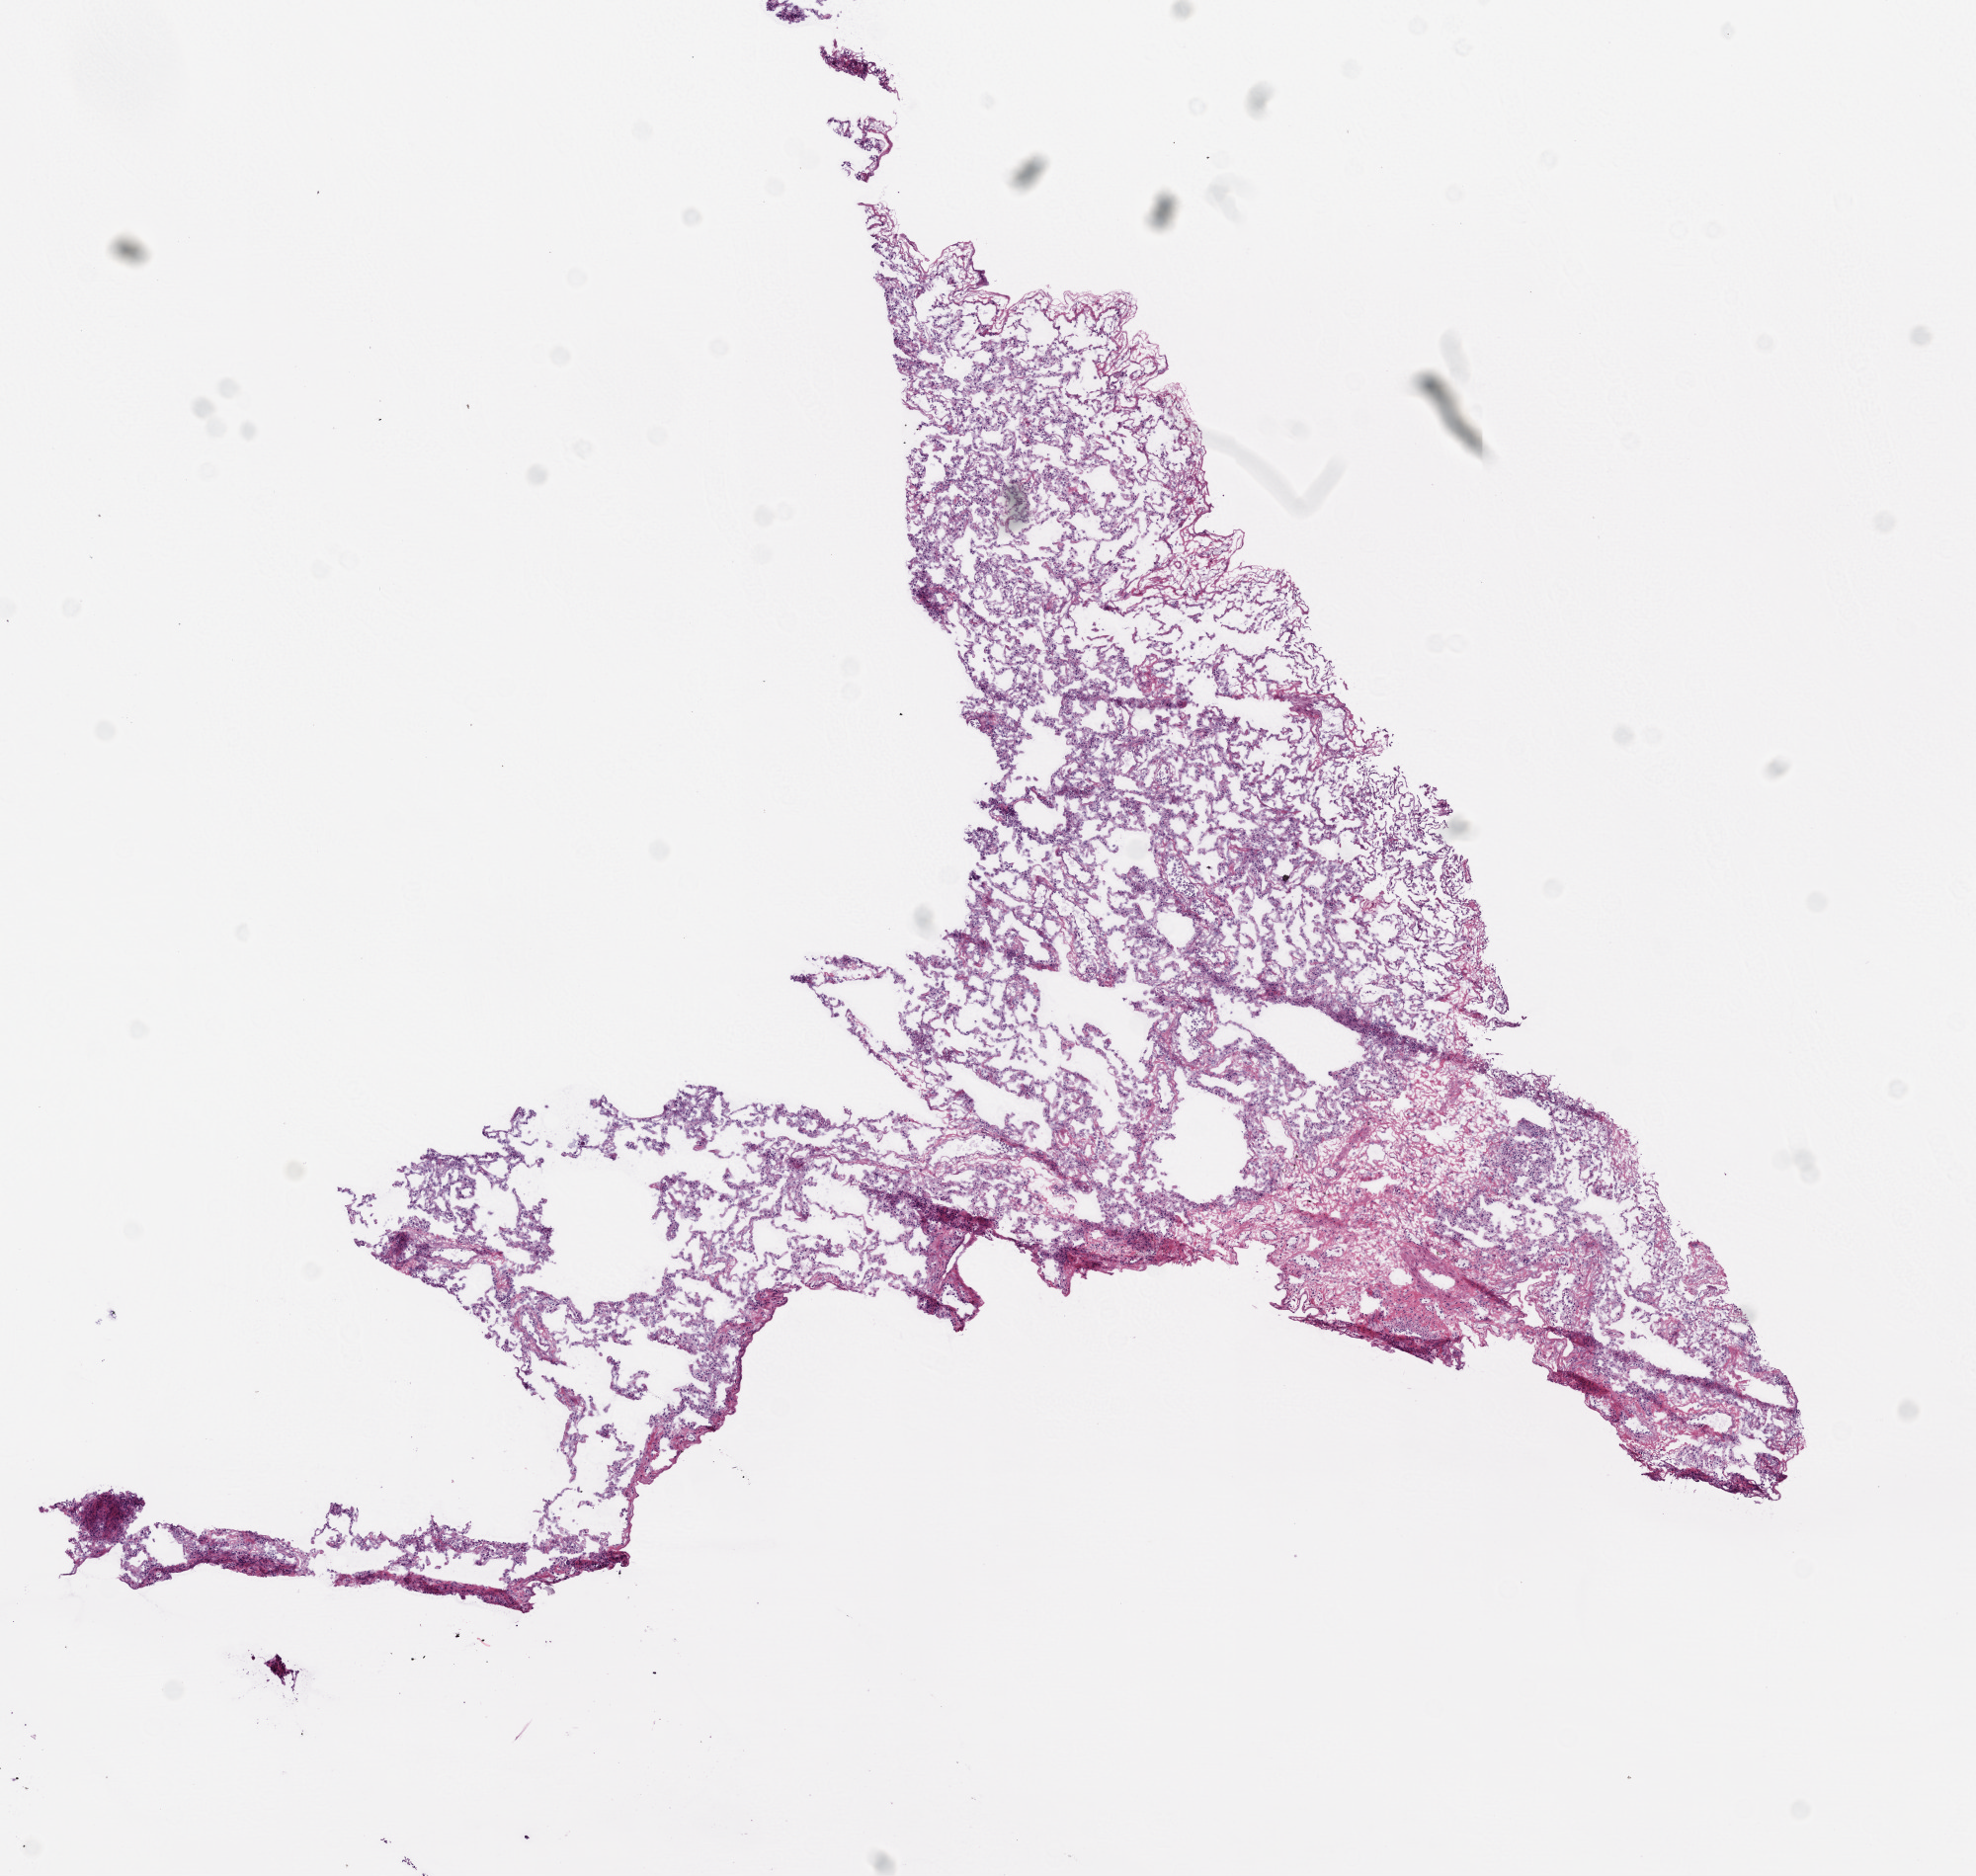
H&E whole-slide image, shown as a low-resolution overview of the whole scanned area (about 8.0 x 7.6 mm); frozen section; sample: solid tissue normal (non-tumour tissue), lung. Female patient; age at initial diagnosis 60 years.
- this section: solid tissue normal (non-tumour) sample from the same patient
- patient diagnosis: Squamous cell carcinoma, NOS (upper lobe, lung)